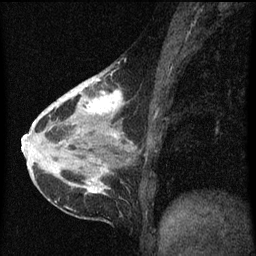
Breast MRI (dynamic contrast-enhanced), one sagittal slice. Position 27 of 60 along the scan axis. Dynamic contrast-enhanced series, image 2 of 3 at this slice position (ordered by acquisition). 1.5 T. TE 4.2 ms, TR 8 ms. 2 mm slice thickness. 256 × 256 image matrix. Female patient, age 38 years.
Structures marked on this image (semi-automatically segmented with operator editing):
- analysis volume of interest (the breast-tissue region the enhancement analysis was run in; not a lesion): bounding box [x1, y1, x2, y2] px = [61, 66, 130, 147]
- tumour enhancement mask (voxels above the 70 % enhancement threshold inside the analysis volume of interest): [62, 76, 124, 139]